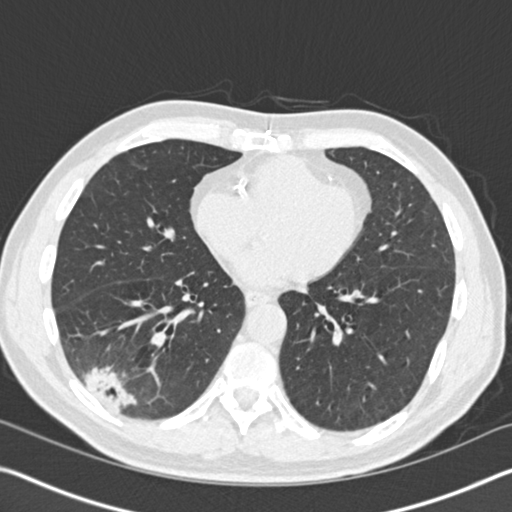
Axial slice from a low-dose chest CT screening exam; baseline annual screen; lung window (W 1500 / L -600 HU); 2 mm slice thickness; 120 kVp; 512 × 512 image matrix, field of view 340 × 340 mm. Male, age 61 years at enrolment.
Expert-annotated lung lesion, bounding box (x1, y1, x2, y2) in pixels: (46, 324, 157, 423). The exam's reader record, not a measurement of the box and not confirmed to be the same lesion: non-calcified nodule or mass ≥4 mm, right lower lobe, 52 × 36 mm, spiculated (stellate) margins, soft tissue attenuation. Official screen result: positive, change unspecified: nodule(s) >= 4 mm or enlarging nodule(s), mass(es), or other non-specific abnormalities suspicious for lung cancer. Lung cancer was diagnosed 392 days after this screen: bronchiolo-alveolar adenocarcinoma, NOS, right lower lobe, moderately differentiated (G2), stage IIIB (AJCC 6th edition), 90 mm at pathology.